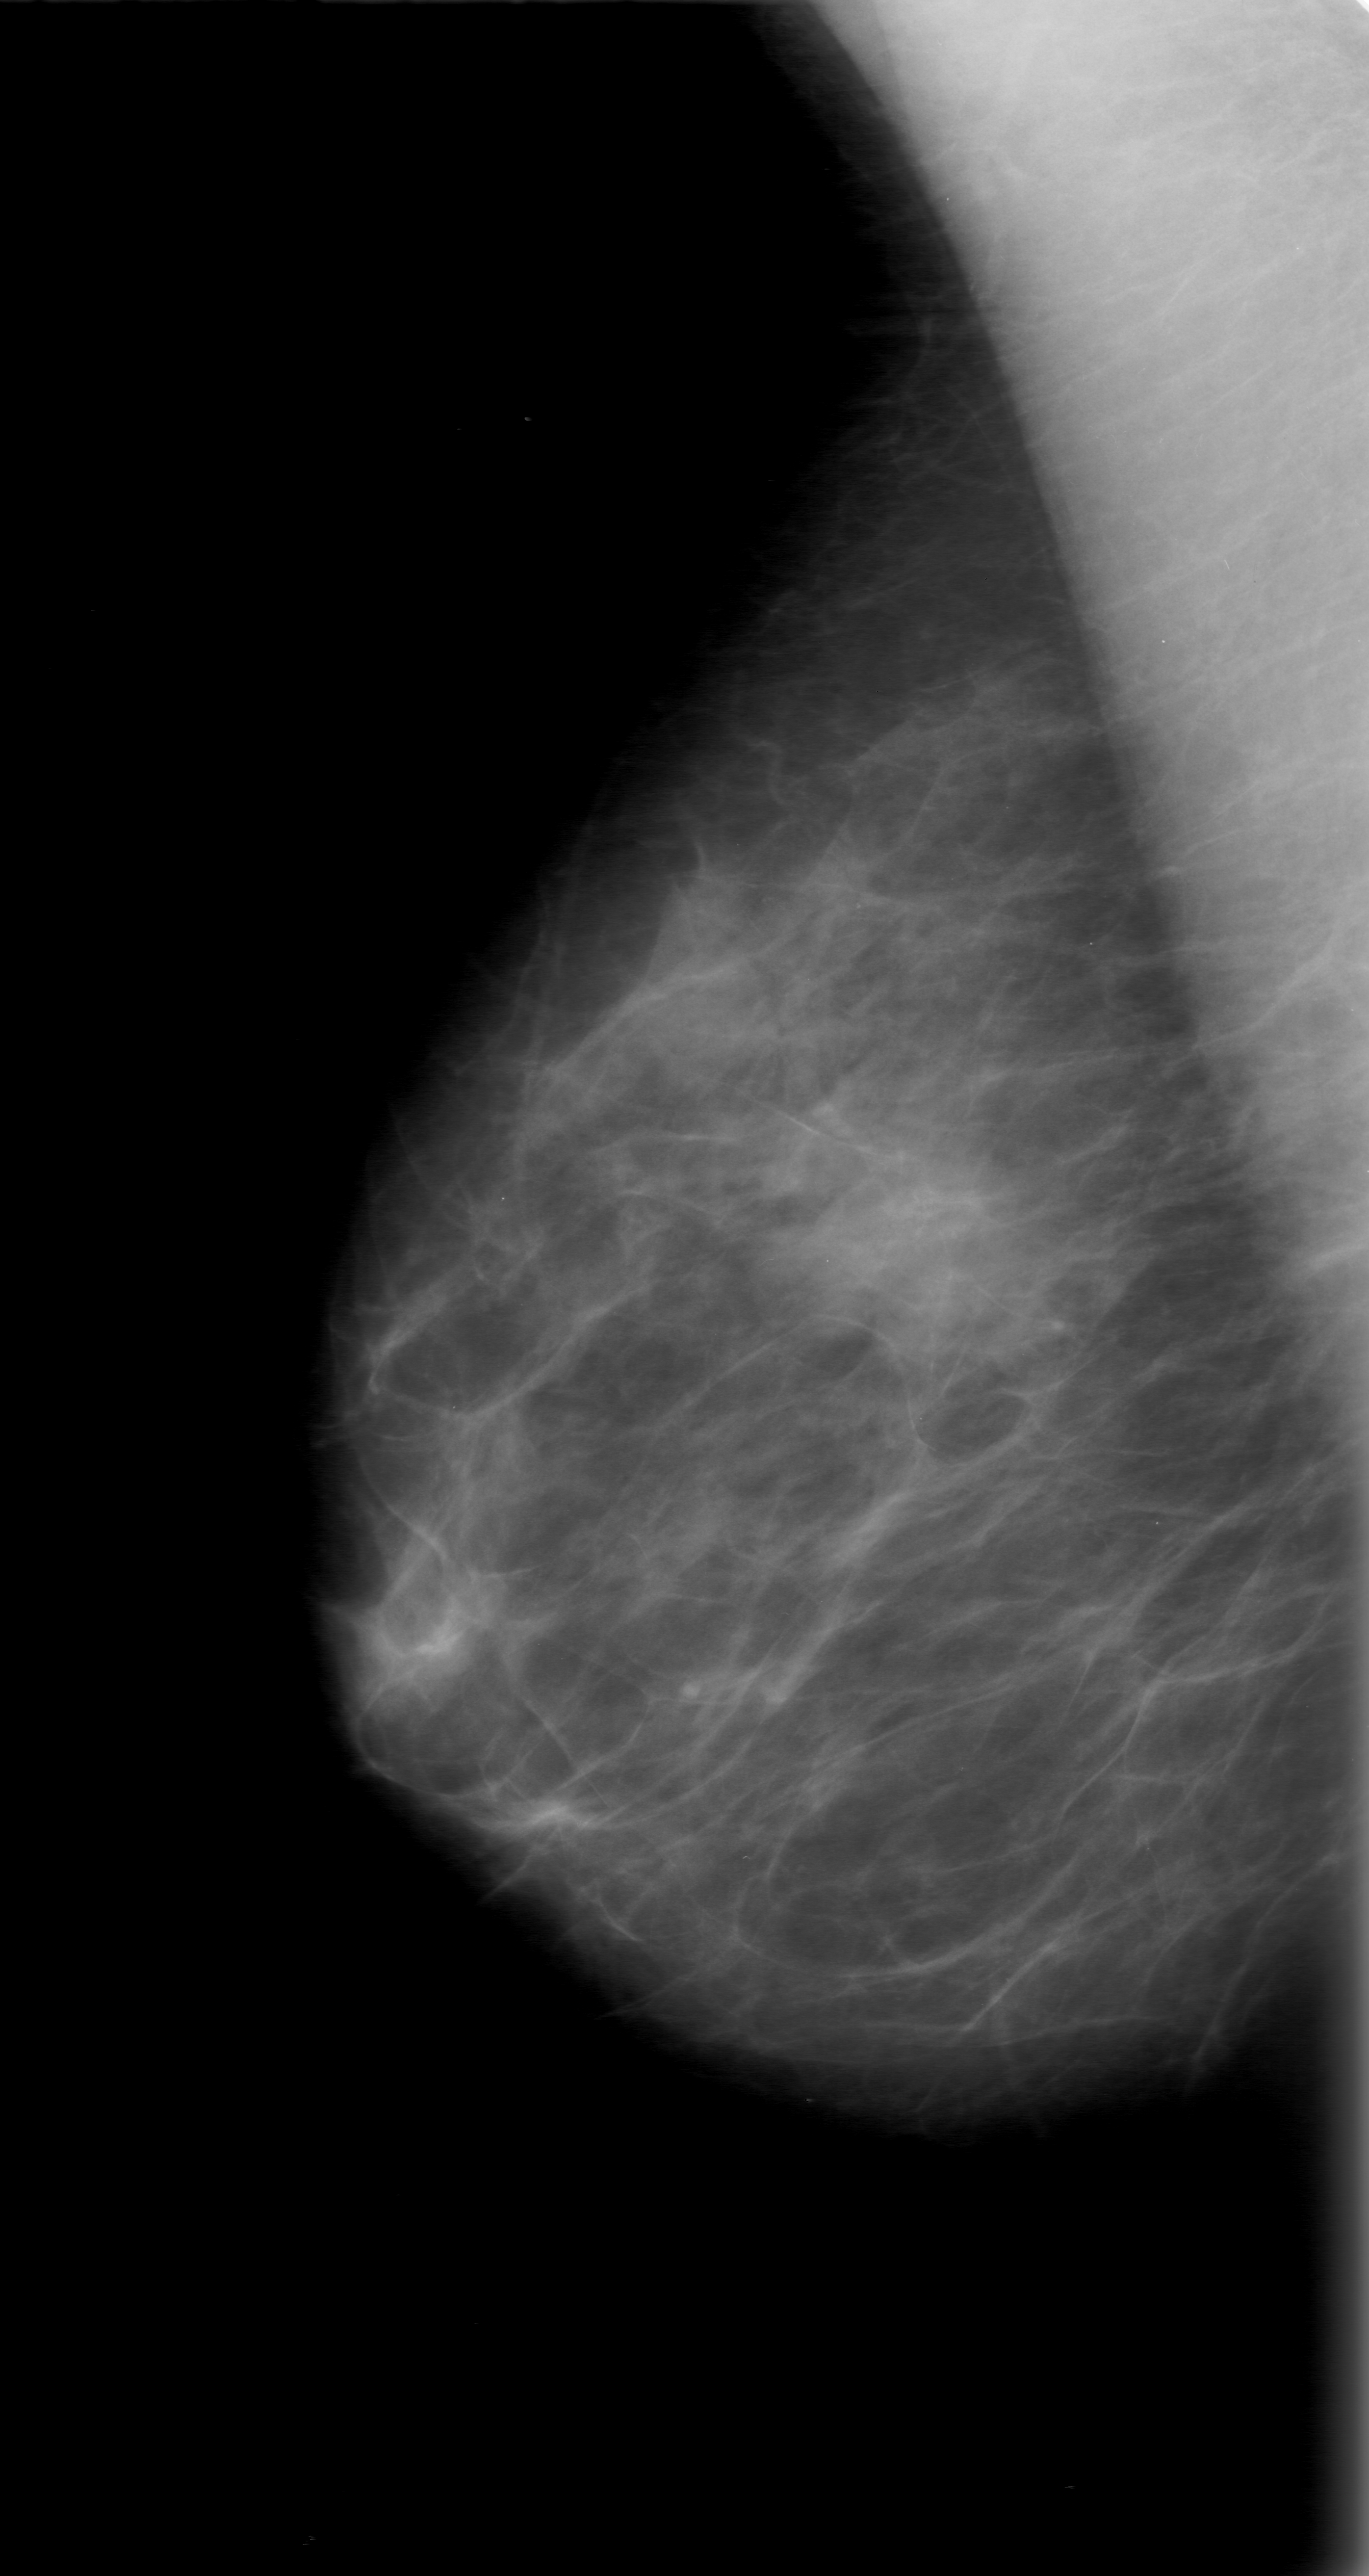
Scanned film-screen mammogram; right breast; mediolateral oblique (MLO) view; breast composition: scattered fibroglandular densities (BI-RADS density category 2 of 4).
Mass, shape oval, margins obscured; BI-RADS assessment category 0 (incomplete: needs additional imaging); pathology (as recorded): benign.